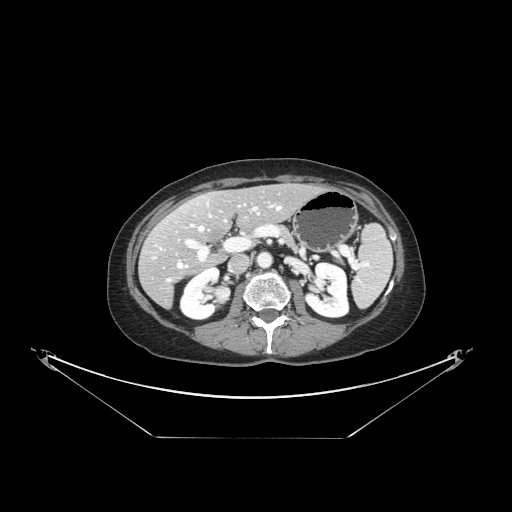
Contrast-enhanced abdominal CT, one axial slice; 120 kVp; intravenous contrast given; soft-tissue window (W 400 / L 40 HU); 512 × 512 image matrix, field of view 500 × 500 mm. Female patient, age 73 years. Case-level facts recorded for this patient, not image findings: diagnosis: colorectal cancer liver metastases, imaged before liver resection; multiple liver metastases: no; largest metastasis: 1 cm; disease in both lobes: no.
Outlined on this slice (expert manual segmentation):
- hepatic veins: bounding box [x1, y1, x2, y2] px = [153, 203, 282, 281]
- liver: [140, 185, 318, 307]
- planned liver remnant (the part of the liver to remain after resection): [168, 184, 319, 243]
- portal vein (with intrahepatic branches): [185, 207, 260, 262]